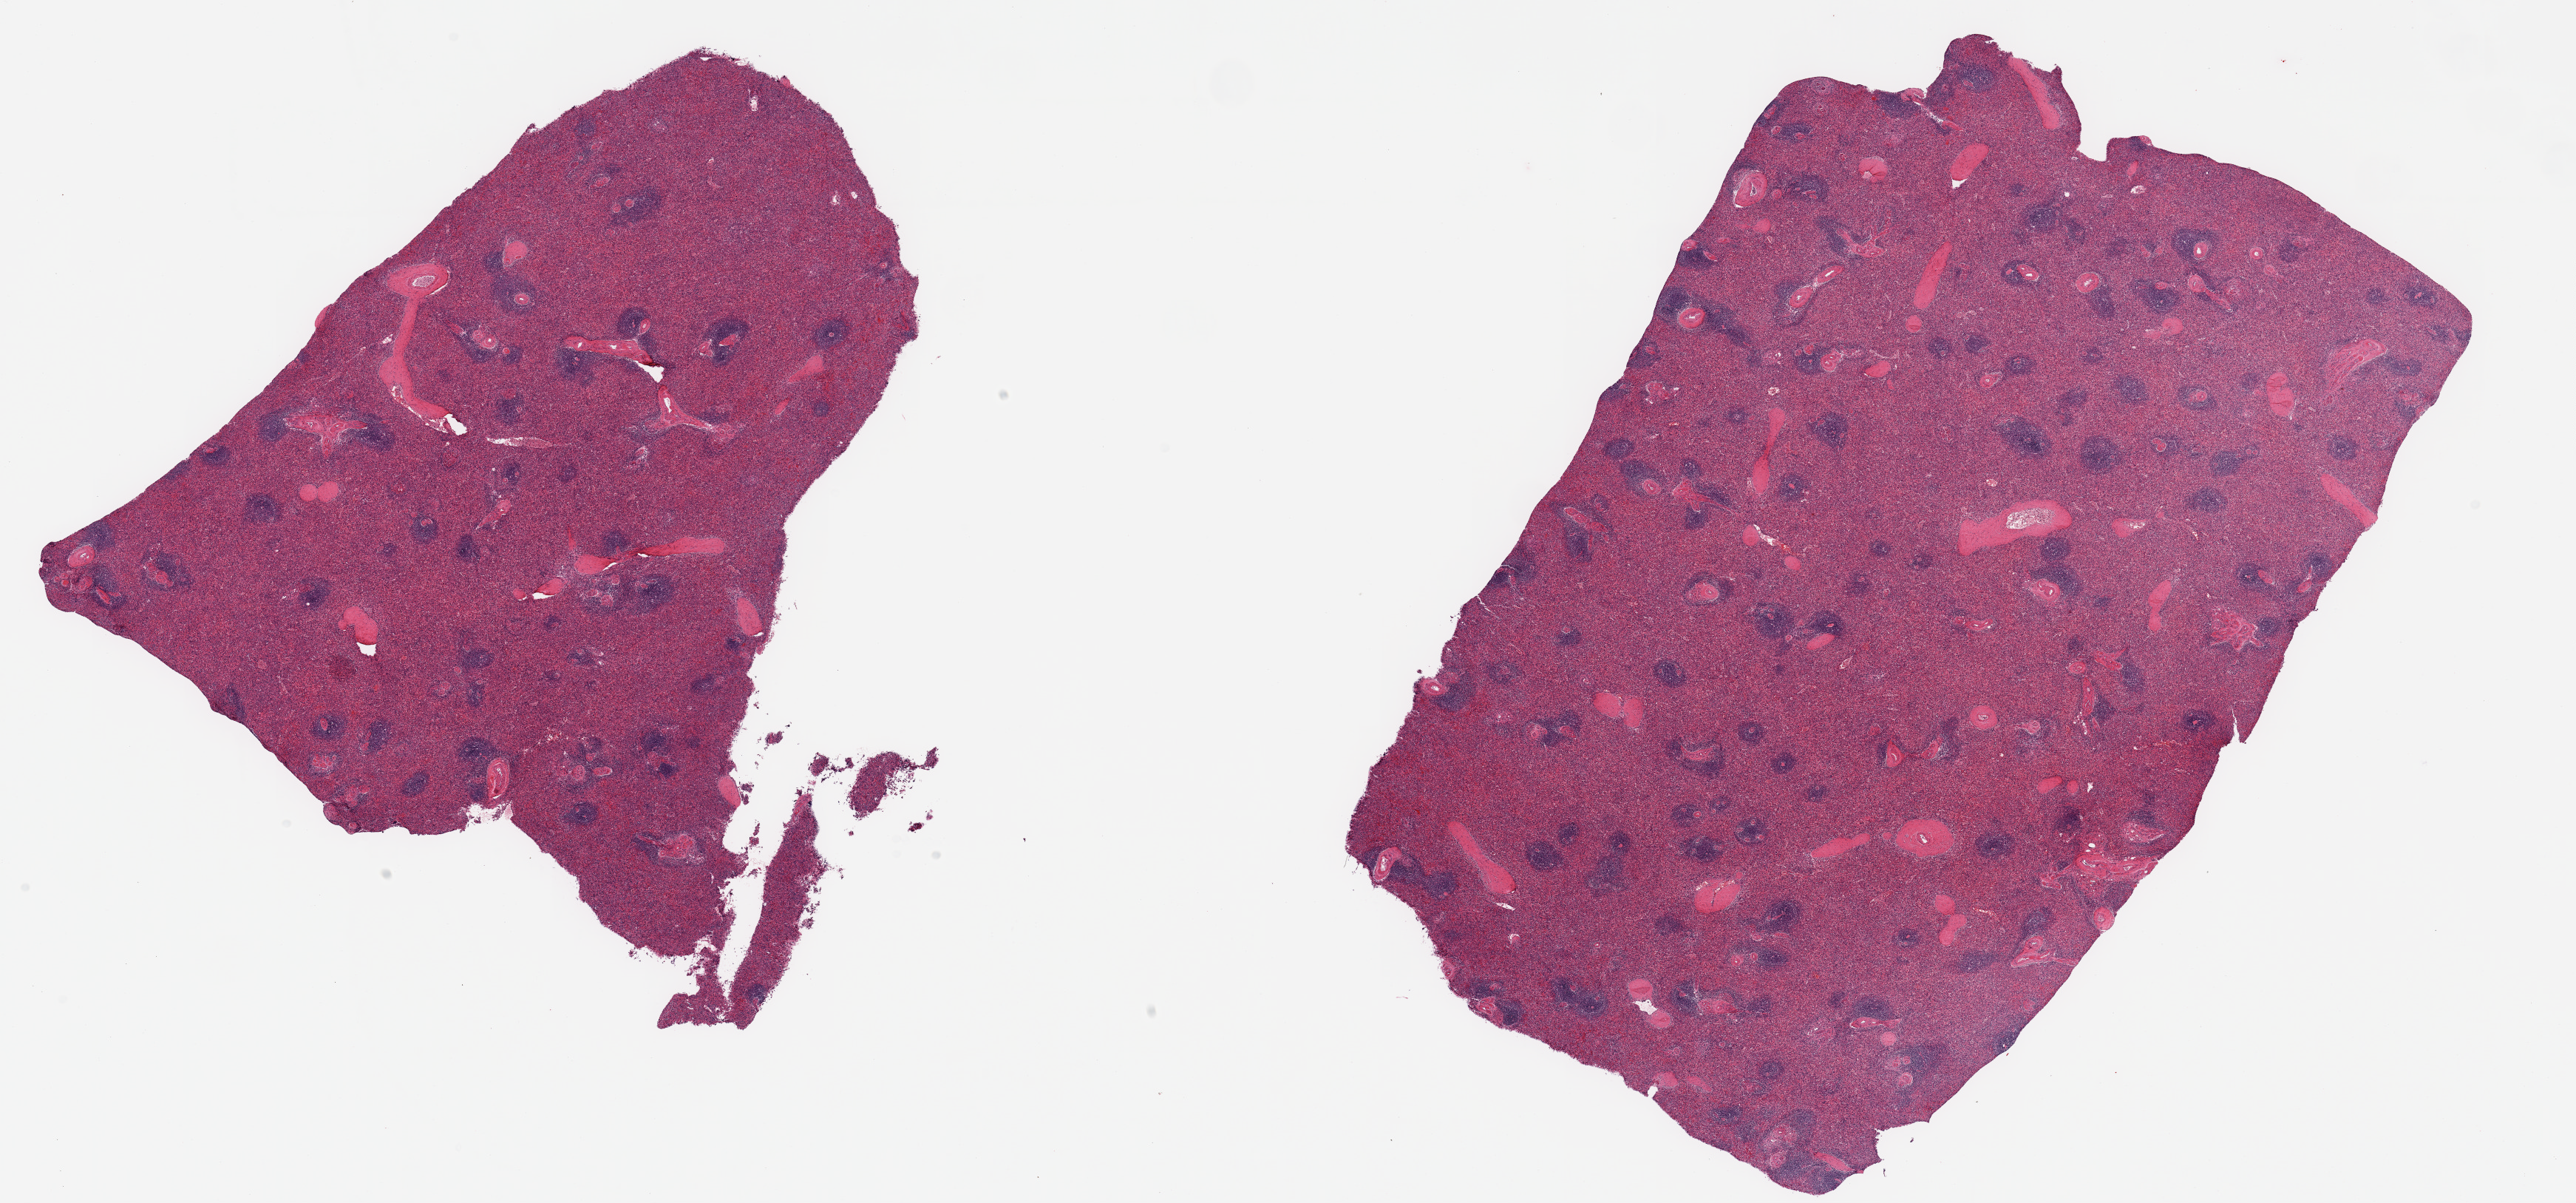
Digitized haematoxylin and eosin-stained section, low-resolution overview of the scanned area, about 27.6 x 12.9 mm, PAXgene-fixed paraffin-embedded (PFPE) section, target tissue: spleen, tissue donor sample. Donor: male.
Pathologist's review note for this sample: 2 pieces, no abnormalities.